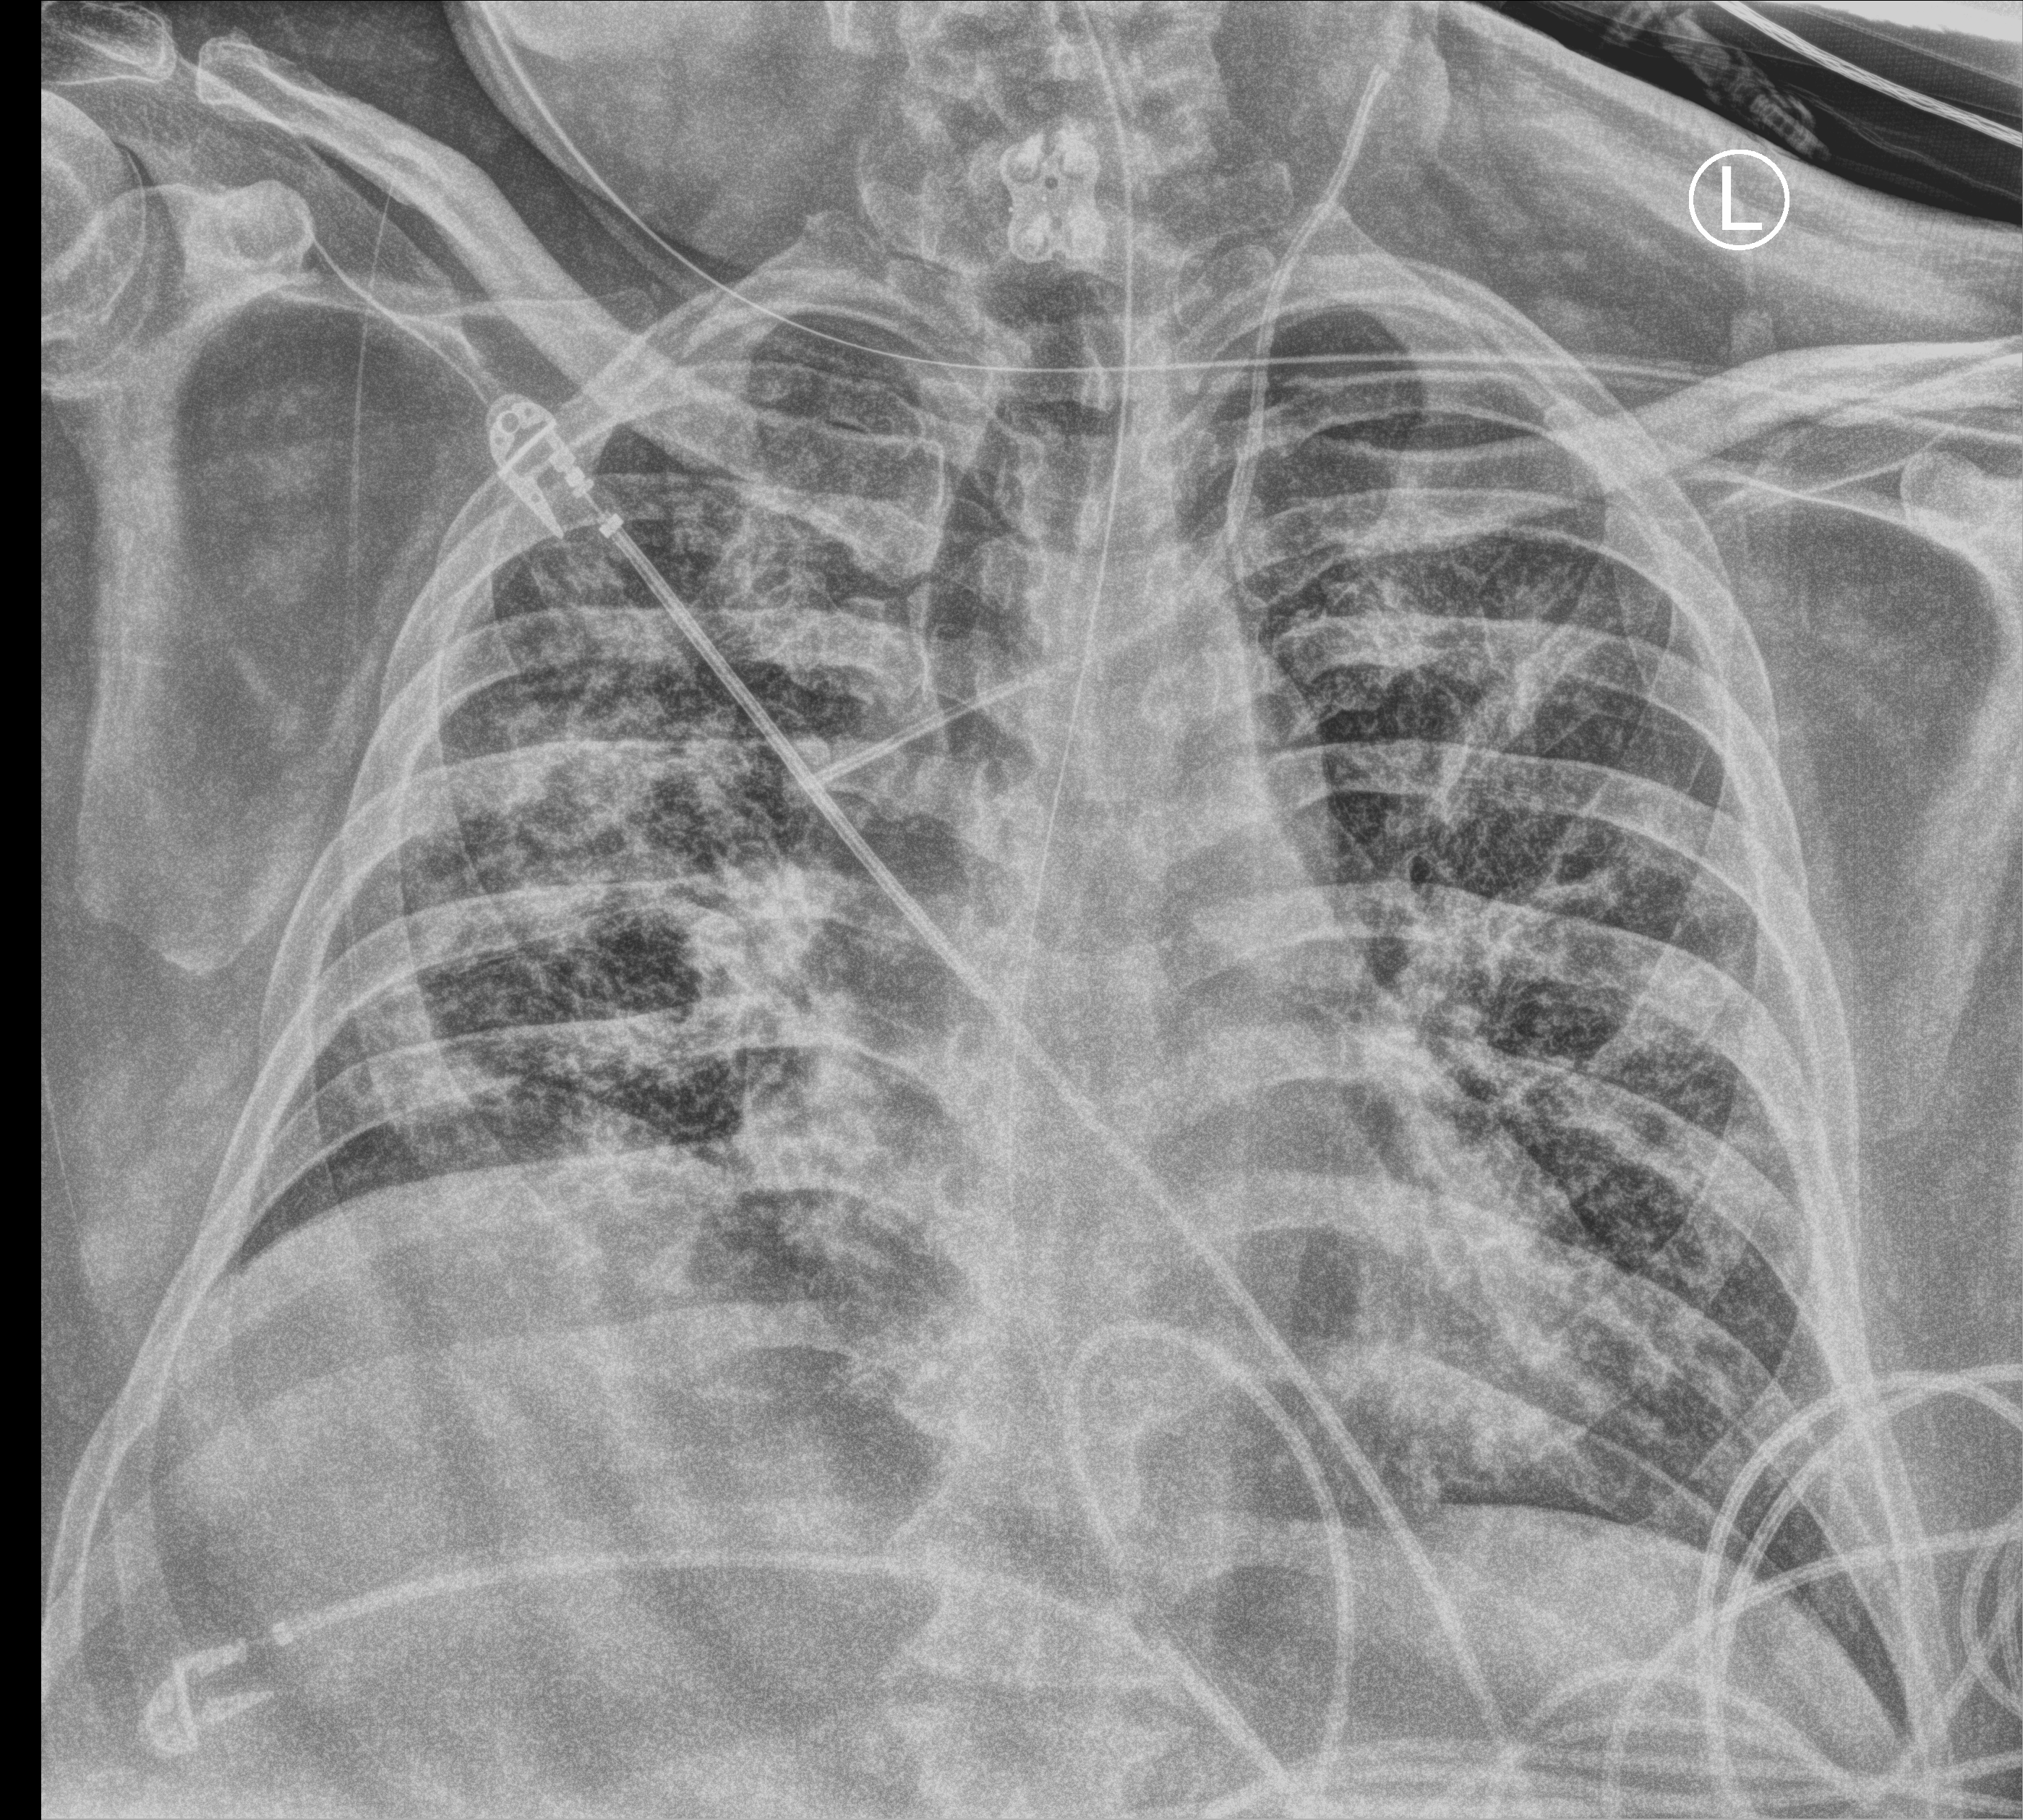
Chest X-ray (portable); anteroposterior (AP) projection. Male patient hospitalised with COVID-19, age 18–59 years.
Admission-level facts for this patient (not findings on this image; timing relative to this image not recorded): chronic kidney disease (admission record): no.